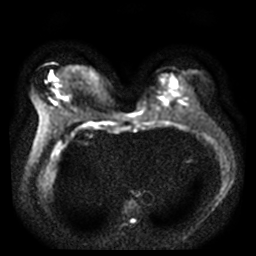
Breast MRI, one axial slice. Slice 16 of 40 in the series (ordered by position). Diffusion-weighted series; image 2 of 4 stored at this slice position (different b-values; order by instance number). 3 T. 5 mm slice thickness. 256 × 256 image matrix, field of view 340 × 340 mm. Female patient.
Annotated regions visible in this slice (manually delineated by an expert):
- tumour on diffusion-weighted imaging: bounding box (x1, y1, x2, y2) in pixels: (49, 73, 55, 80)